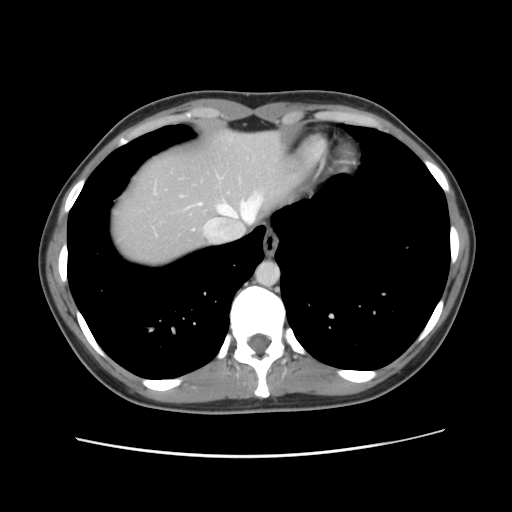
Contrast-enhanced abdominal CT, one axial slice. Position 110 of 134 along the scan axis. 120 kVp. Soft-tissue window (W 400 / L 40 HU). 2.5 mm slice thickness. 512 × 512 image matrix. Female patient, age 33 years. Case-level facts recorded for this patient, not image findings: diagnosis: colorectal cancer liver metastases, imaged before liver resection; multiple liver metastases: yes; largest metastasis: 4.5 cm; disease in both lobes: yes.
Annotated regions visible in this slice (outlined manually by an expert reader):
- hepatic veins: box from (x=195, y=194) to (x=263, y=234) px
- liver: (x=110, y=131)–(x=305, y=266)
- planned liver remnant (the part of the liver to remain after resection): (x=110, y=131)–(x=305, y=266)